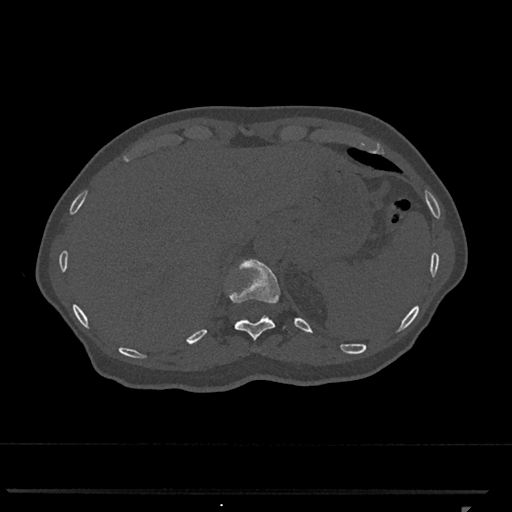
CT including the spine, one axial slice. Position 510 of 793 along the scan axis. Reconstruction kernel Br40s/3. 120 kVp. Bone window (W 1800 / L 400 HU). 512 × 512 image matrix. Patient: female, 62 years. From the clinical record (not read from this slice): primary cancer: renal.
Annotated regions visible in this slice (semi-automatic segmentation, software-assisted and operator-edited):
- T11 vertebra: box from (x=230, y=259) to (x=280, y=341) px